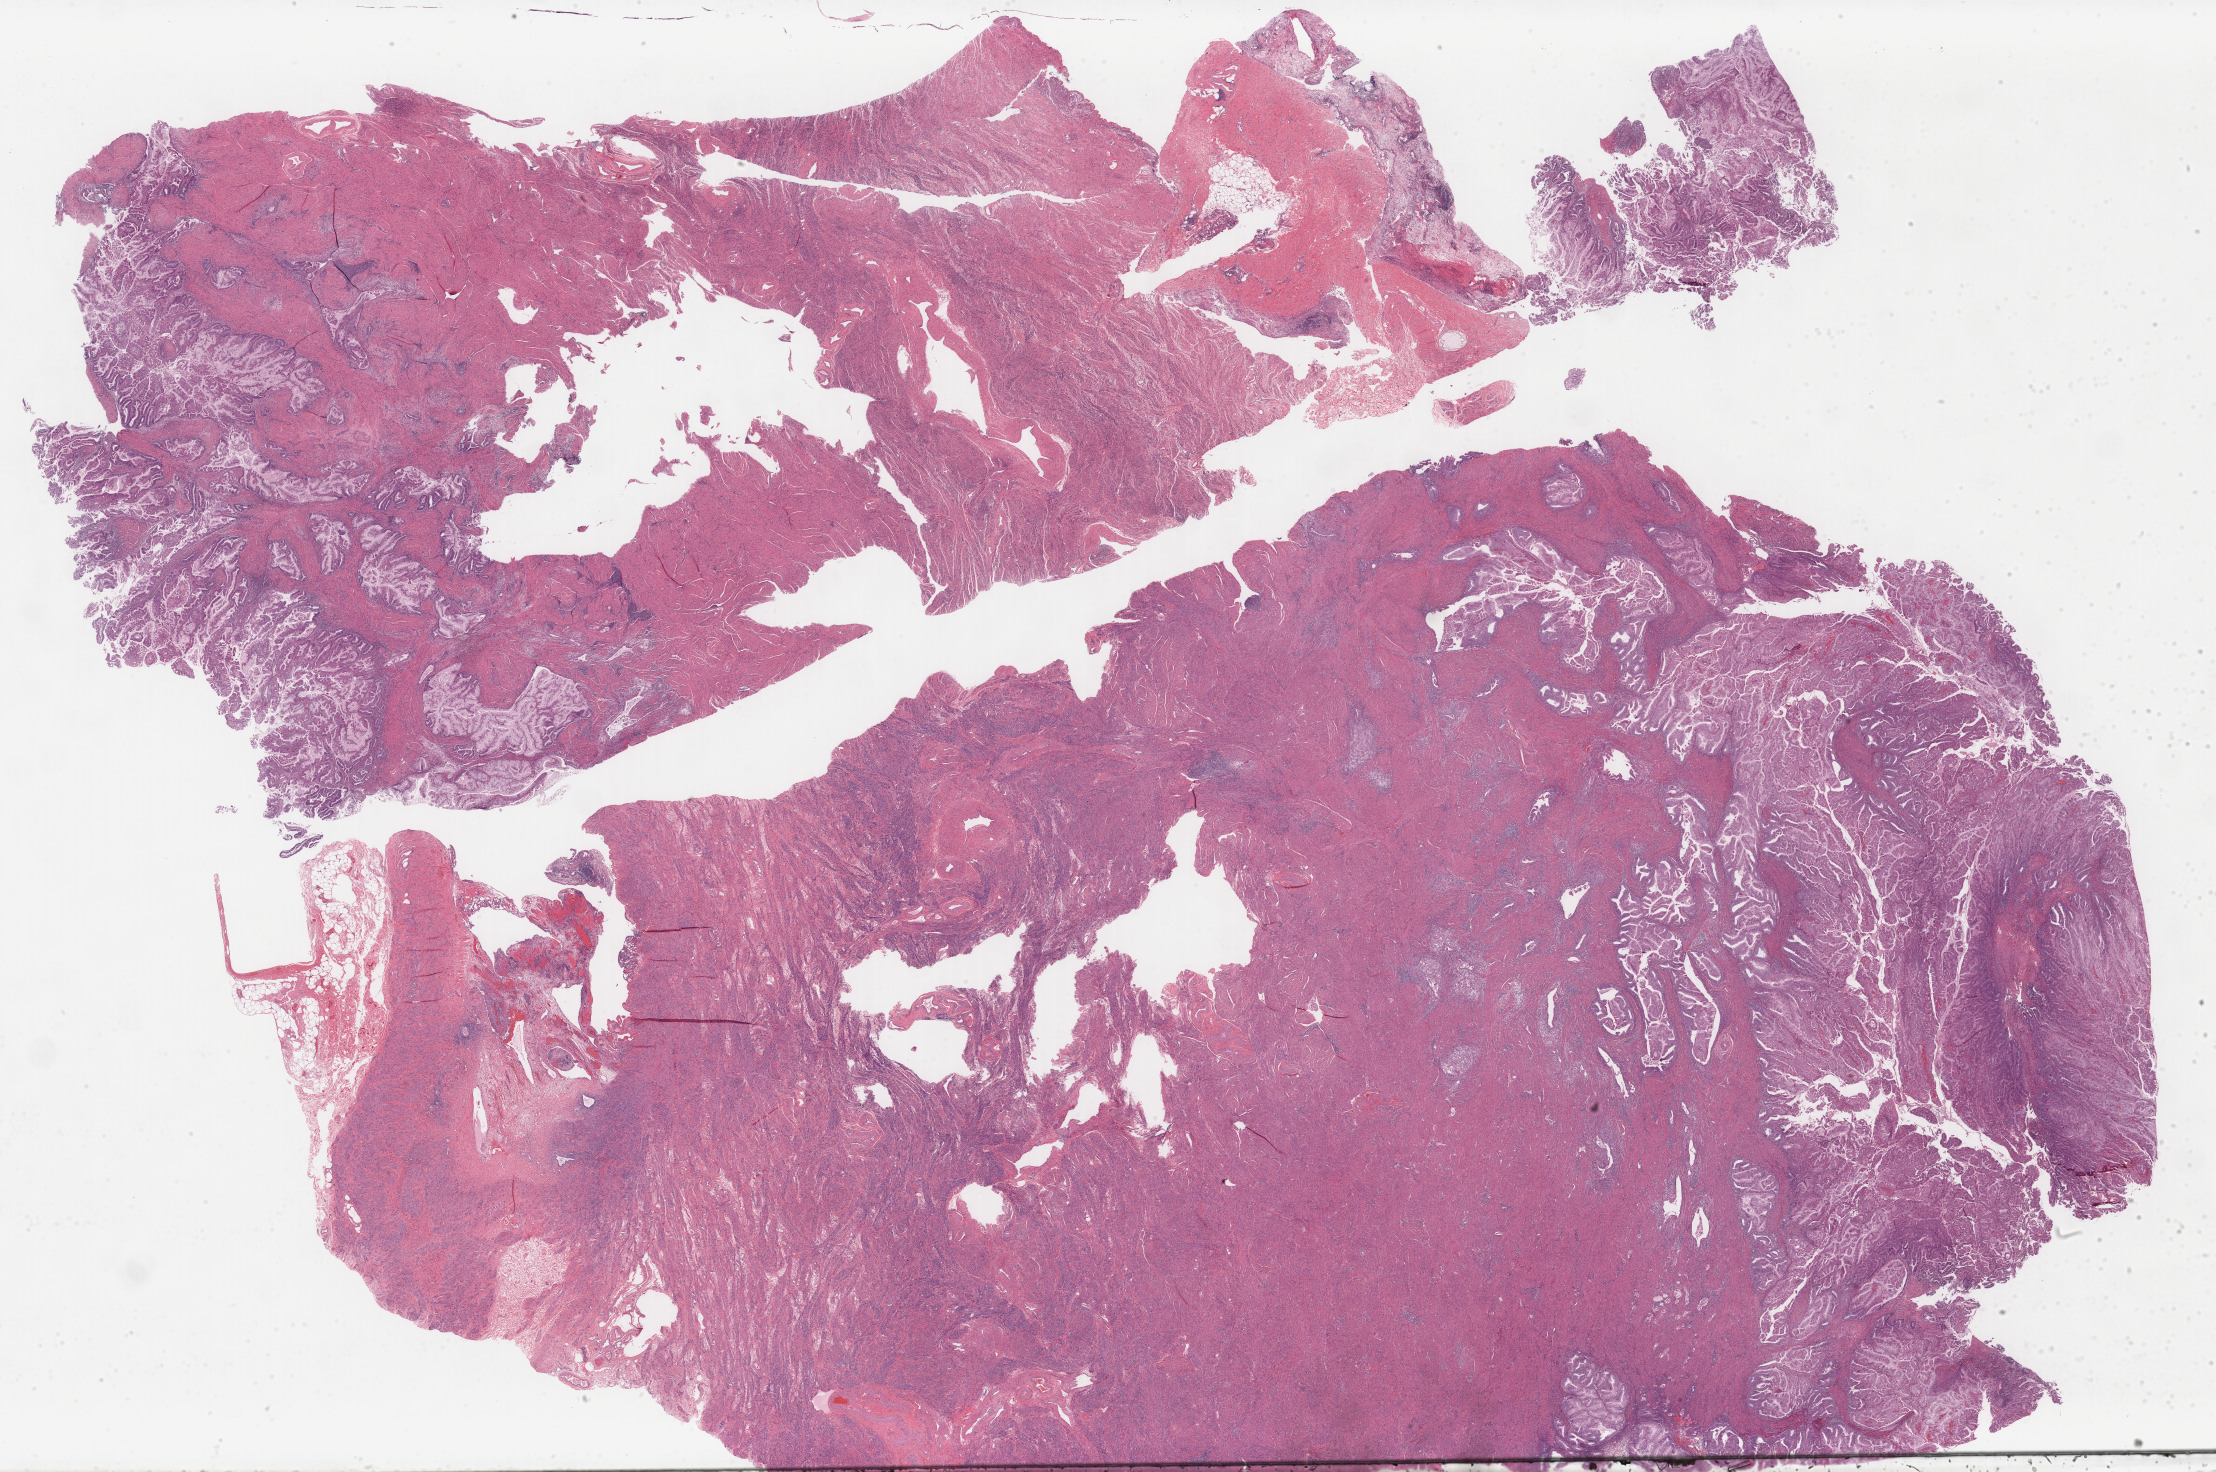
H&E whole-slide image, low-resolution overview of the scanned area, about 35.2 x 23.4 mm (from a 40x scan); formalin-fixed paraffin-embedded (FFPE) diagnostic section; uterus, primary tumour sample. Female patient; age at initial diagnosis 58 years. Histologic grade: G1 (well differentiated).
Diagnosis: Endometrioid adenocarcinoma, NOS (endometrium). FIGO stage: IIIC.